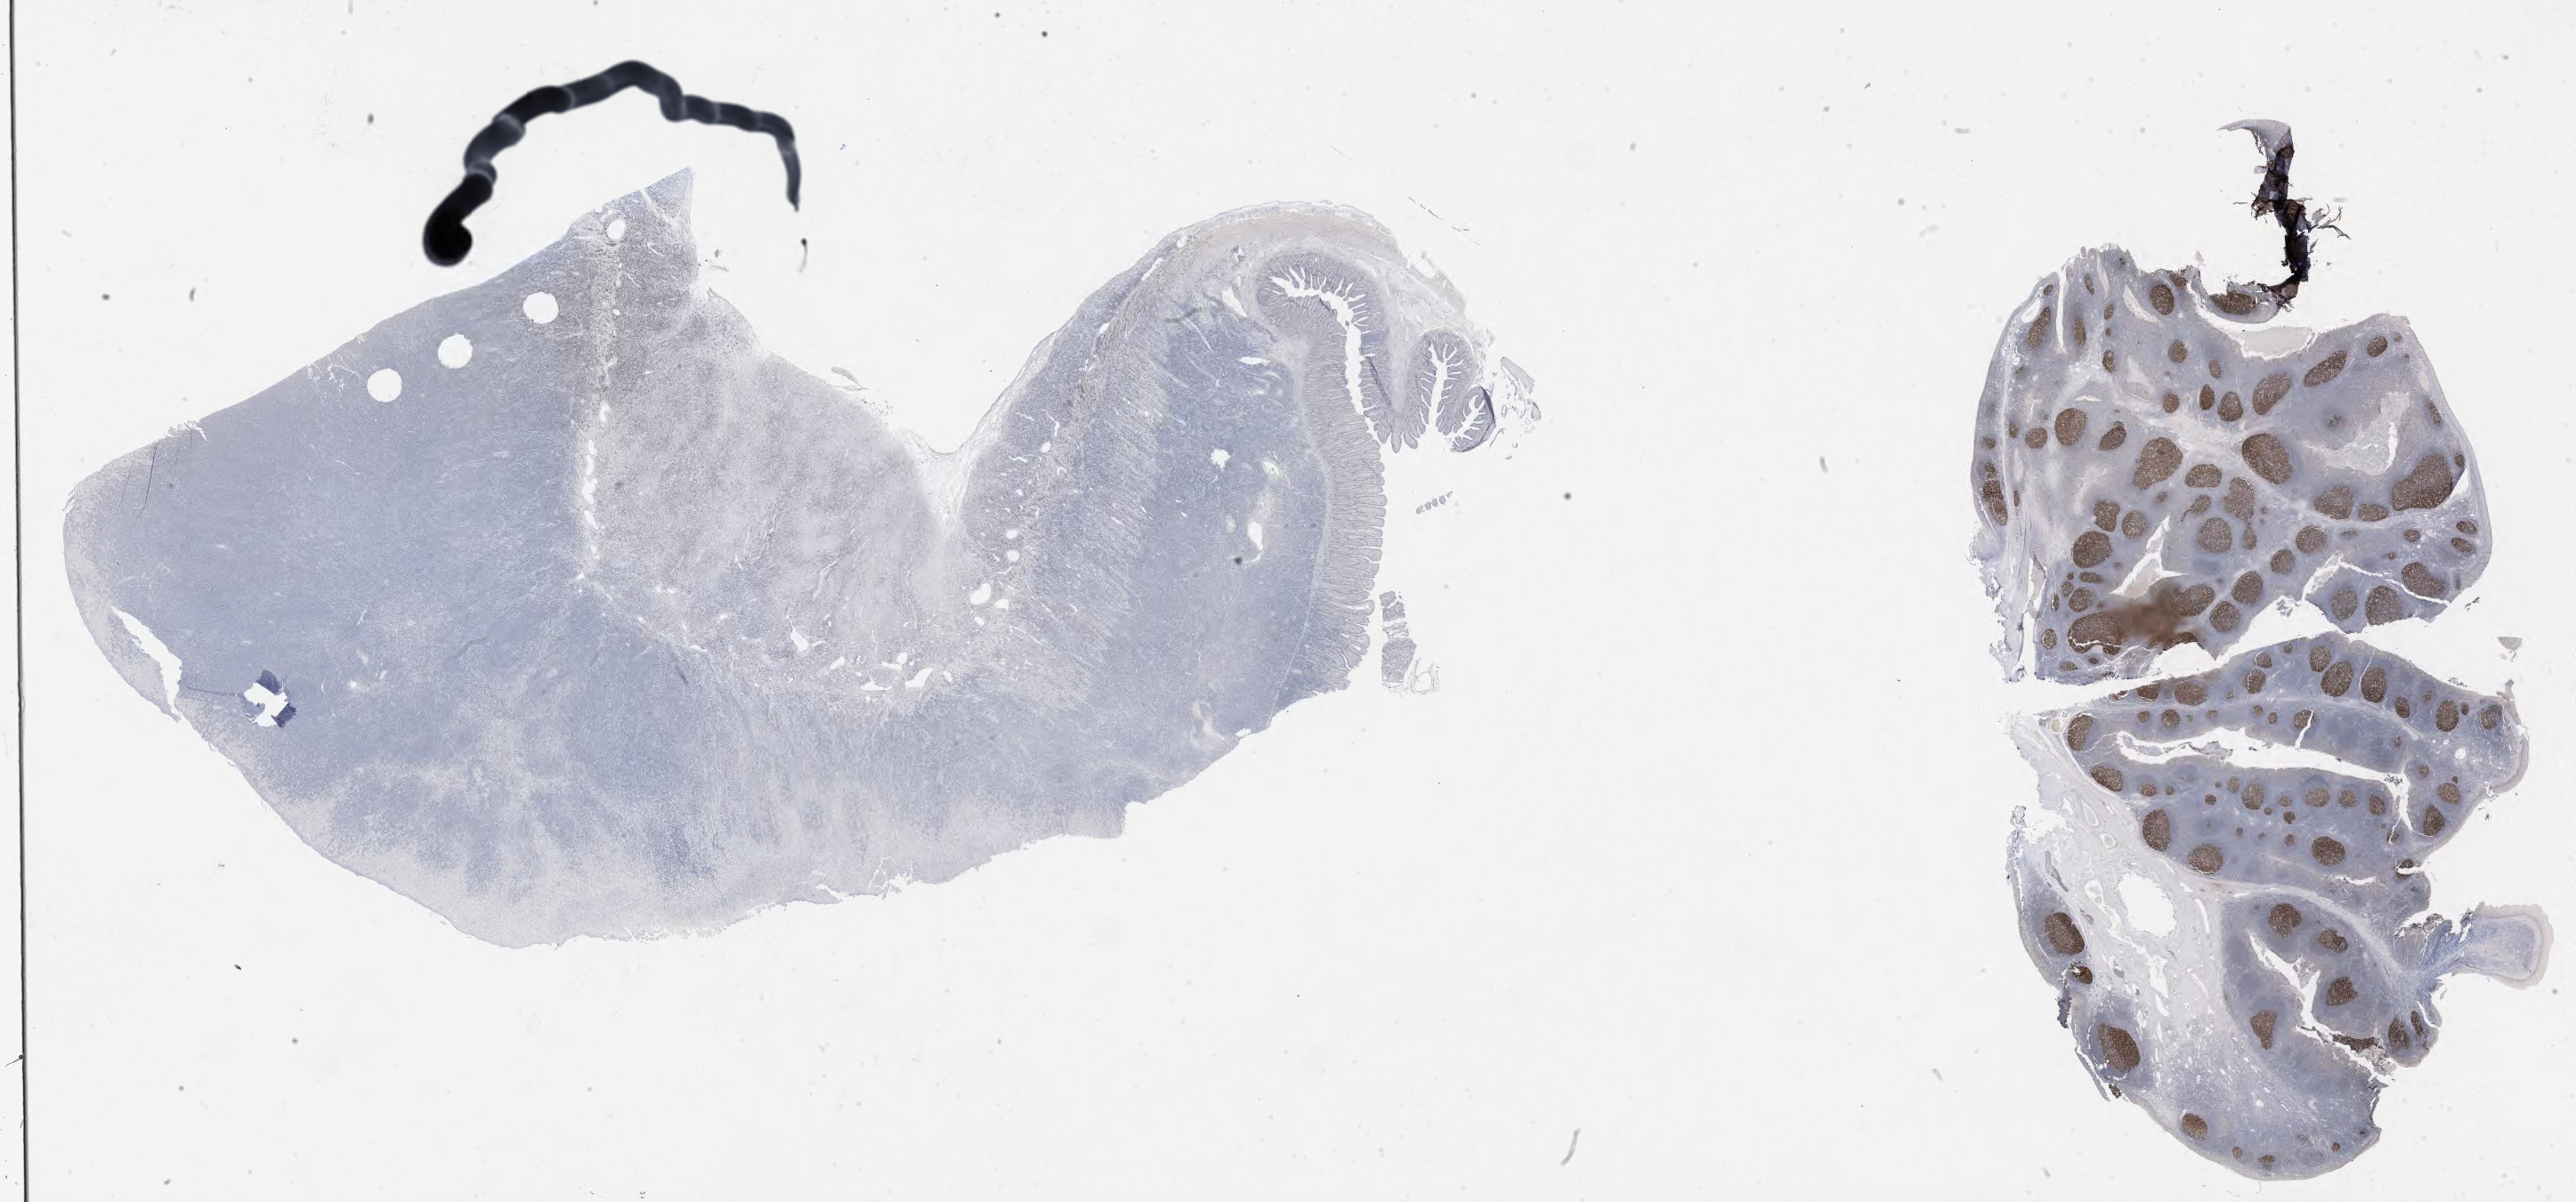
Whole-slide image, immunohistochemical stain for BCL6 — whole scanned area (about 46.8 x 21.8 mm) shown as a low-resolution overview, tumor tissue. Patient: male, age at initial diagnosis 4 years.
* diagnosis: Burkitt lymphoma, NOS